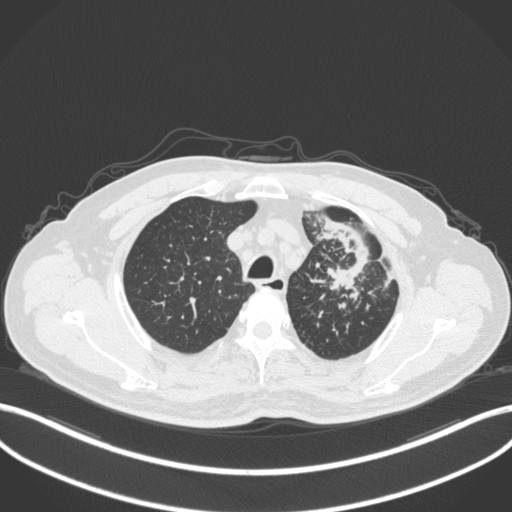
Chest CT, one axial slice. Slice 291 of 386 in the series (ordered by position). Reconstruction kernel B31f. Lung window (W 1500 / L -600 HU). 1 mm slice thickness. 512 × 512 image matrix, field of view 400 × 400 mm. Patient: male, 69 years. From the clinical record (not read from this slice): clinical TNM (as recorded): T2a N2 M0; histopathological grade: G2-3.
Structures marked on this image (bounding box drawn by a radiologist):
- lung tumour (recorded histology: adenocarcinoma): bounding box <315,217,372,295> (left, top, right, bottom; pixels)